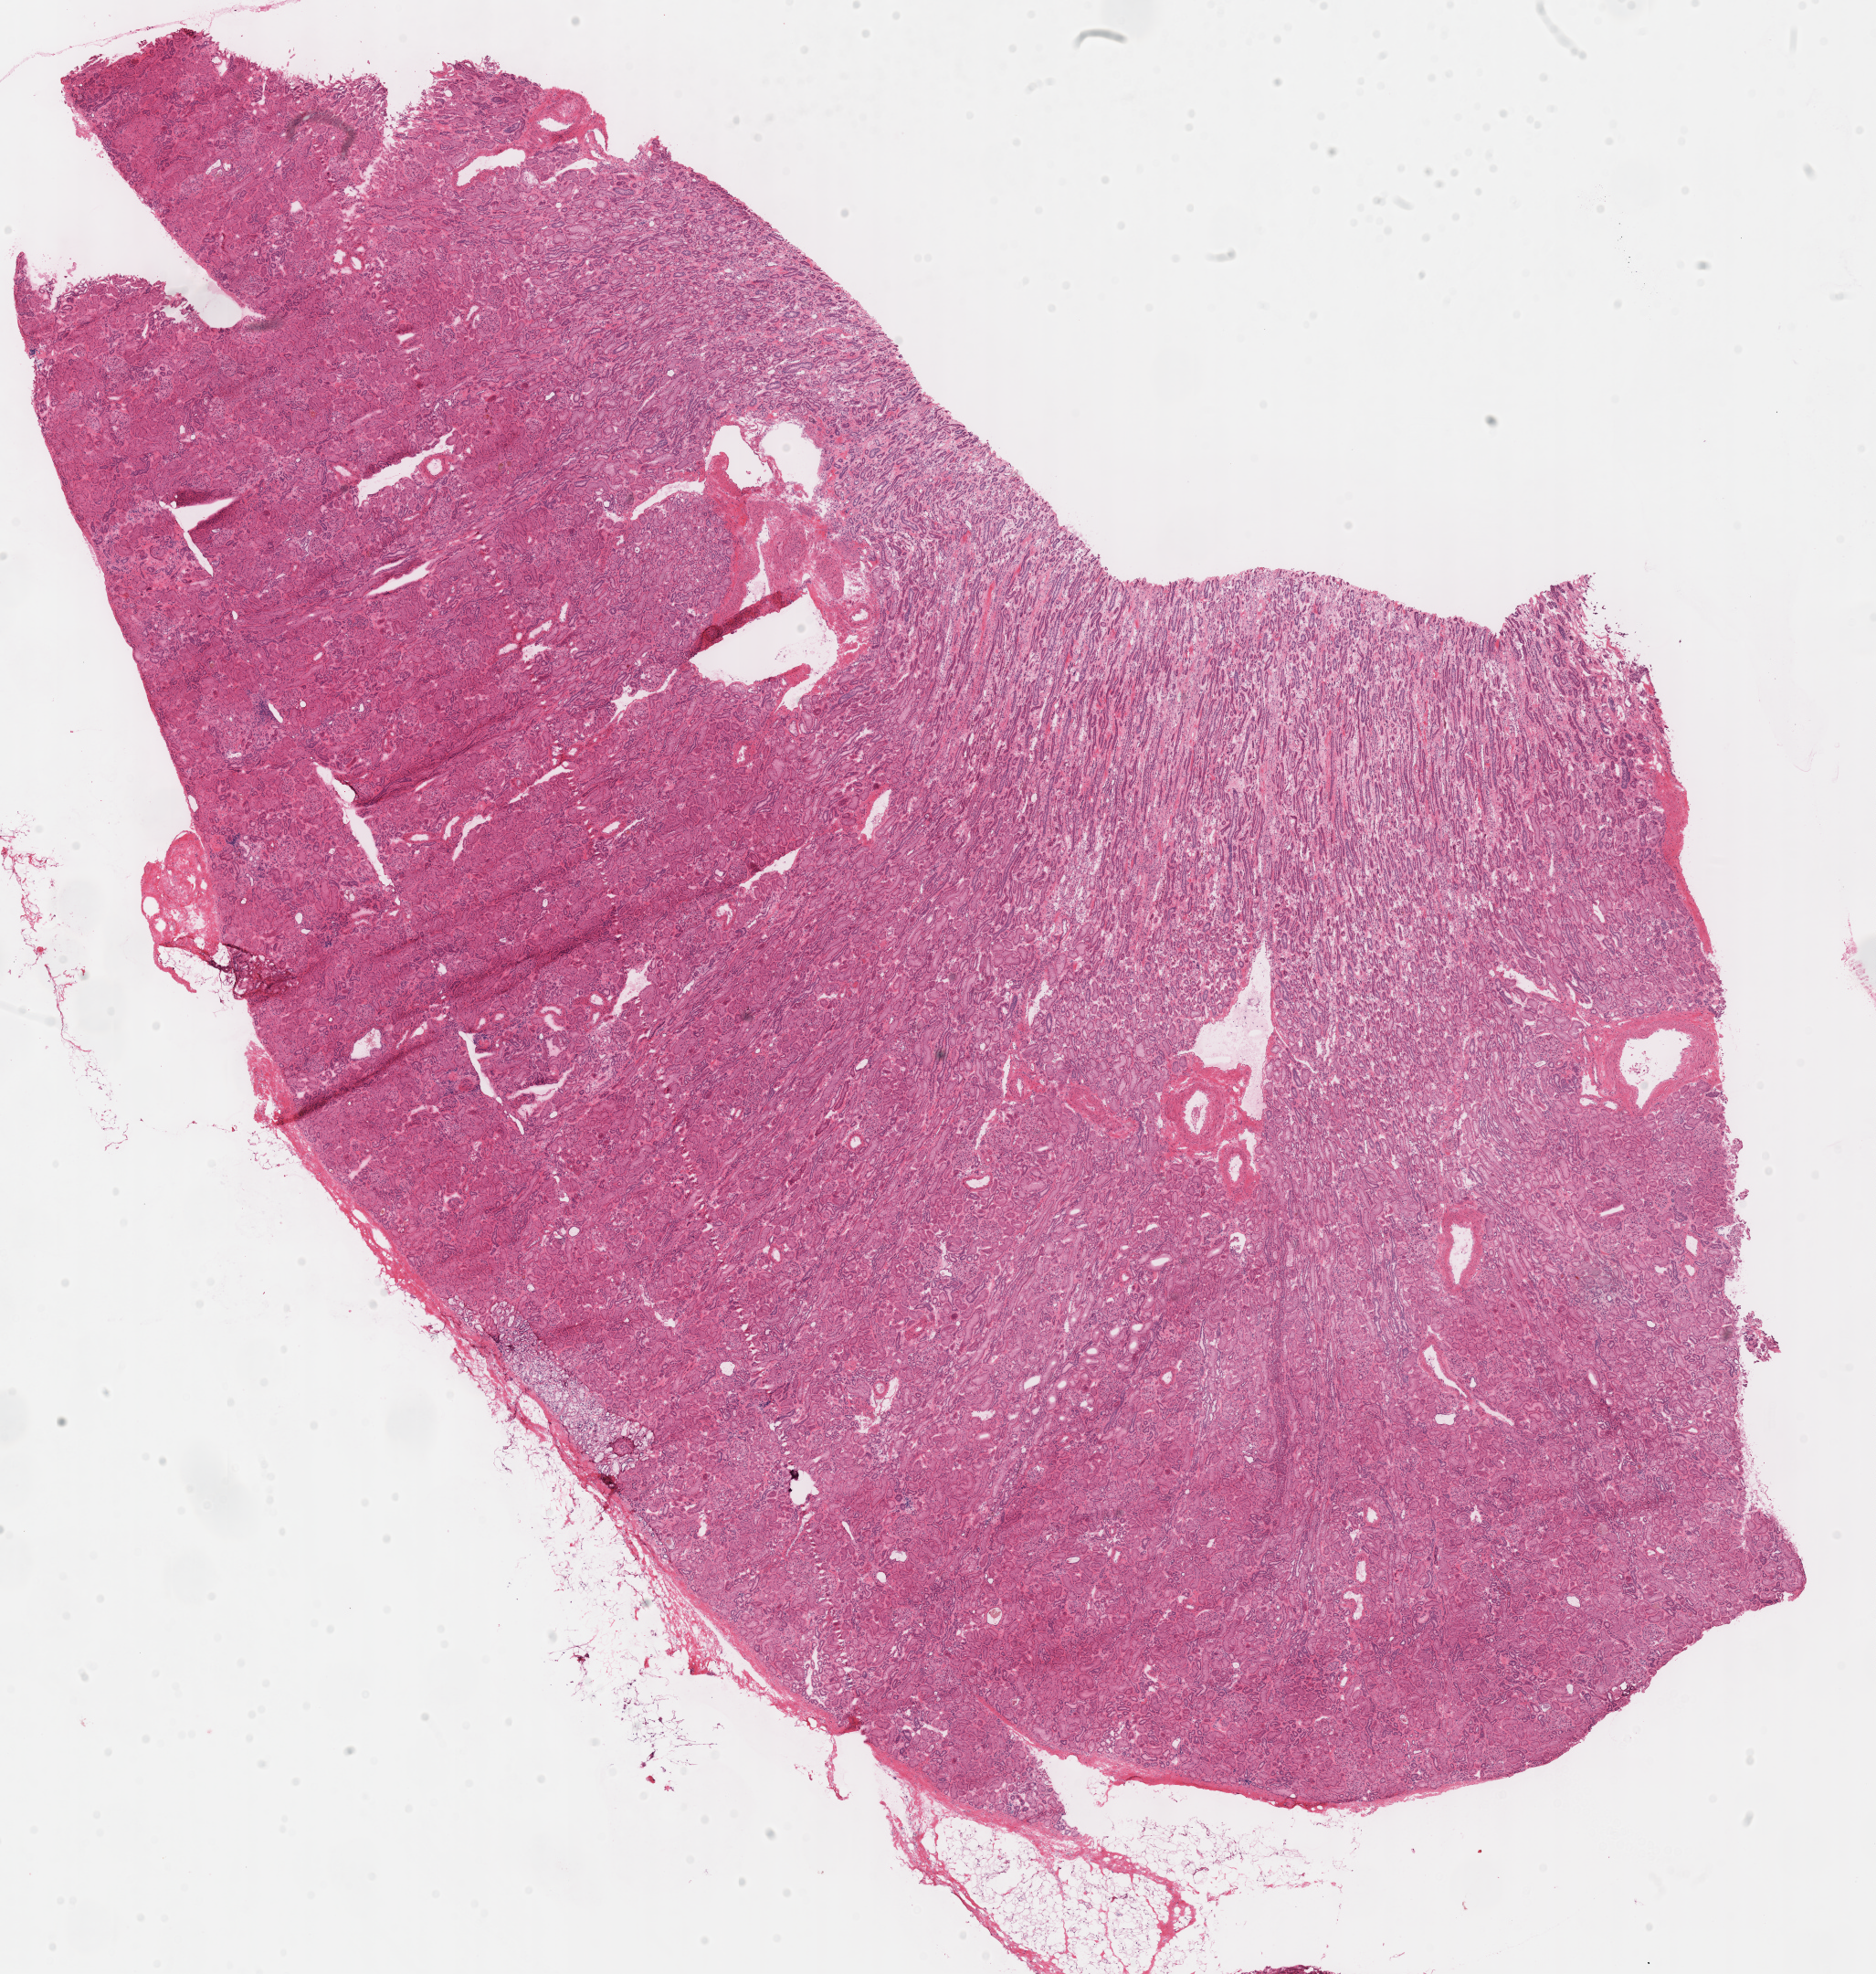
Digitized H&E tissue section (whole slide), low-resolution overview of the scanned area, about 16.2 x 17.0 mm (acquisition: 40x scan); frozen section; sample: solid tissue normal (non-tumour tissue), kidney. Male, age 60 years at initial diagnosis.
This section: solid tissue normal sample (biorepository sample class). Patient diagnosis: Renal cell carcinoma, chromophobe type.